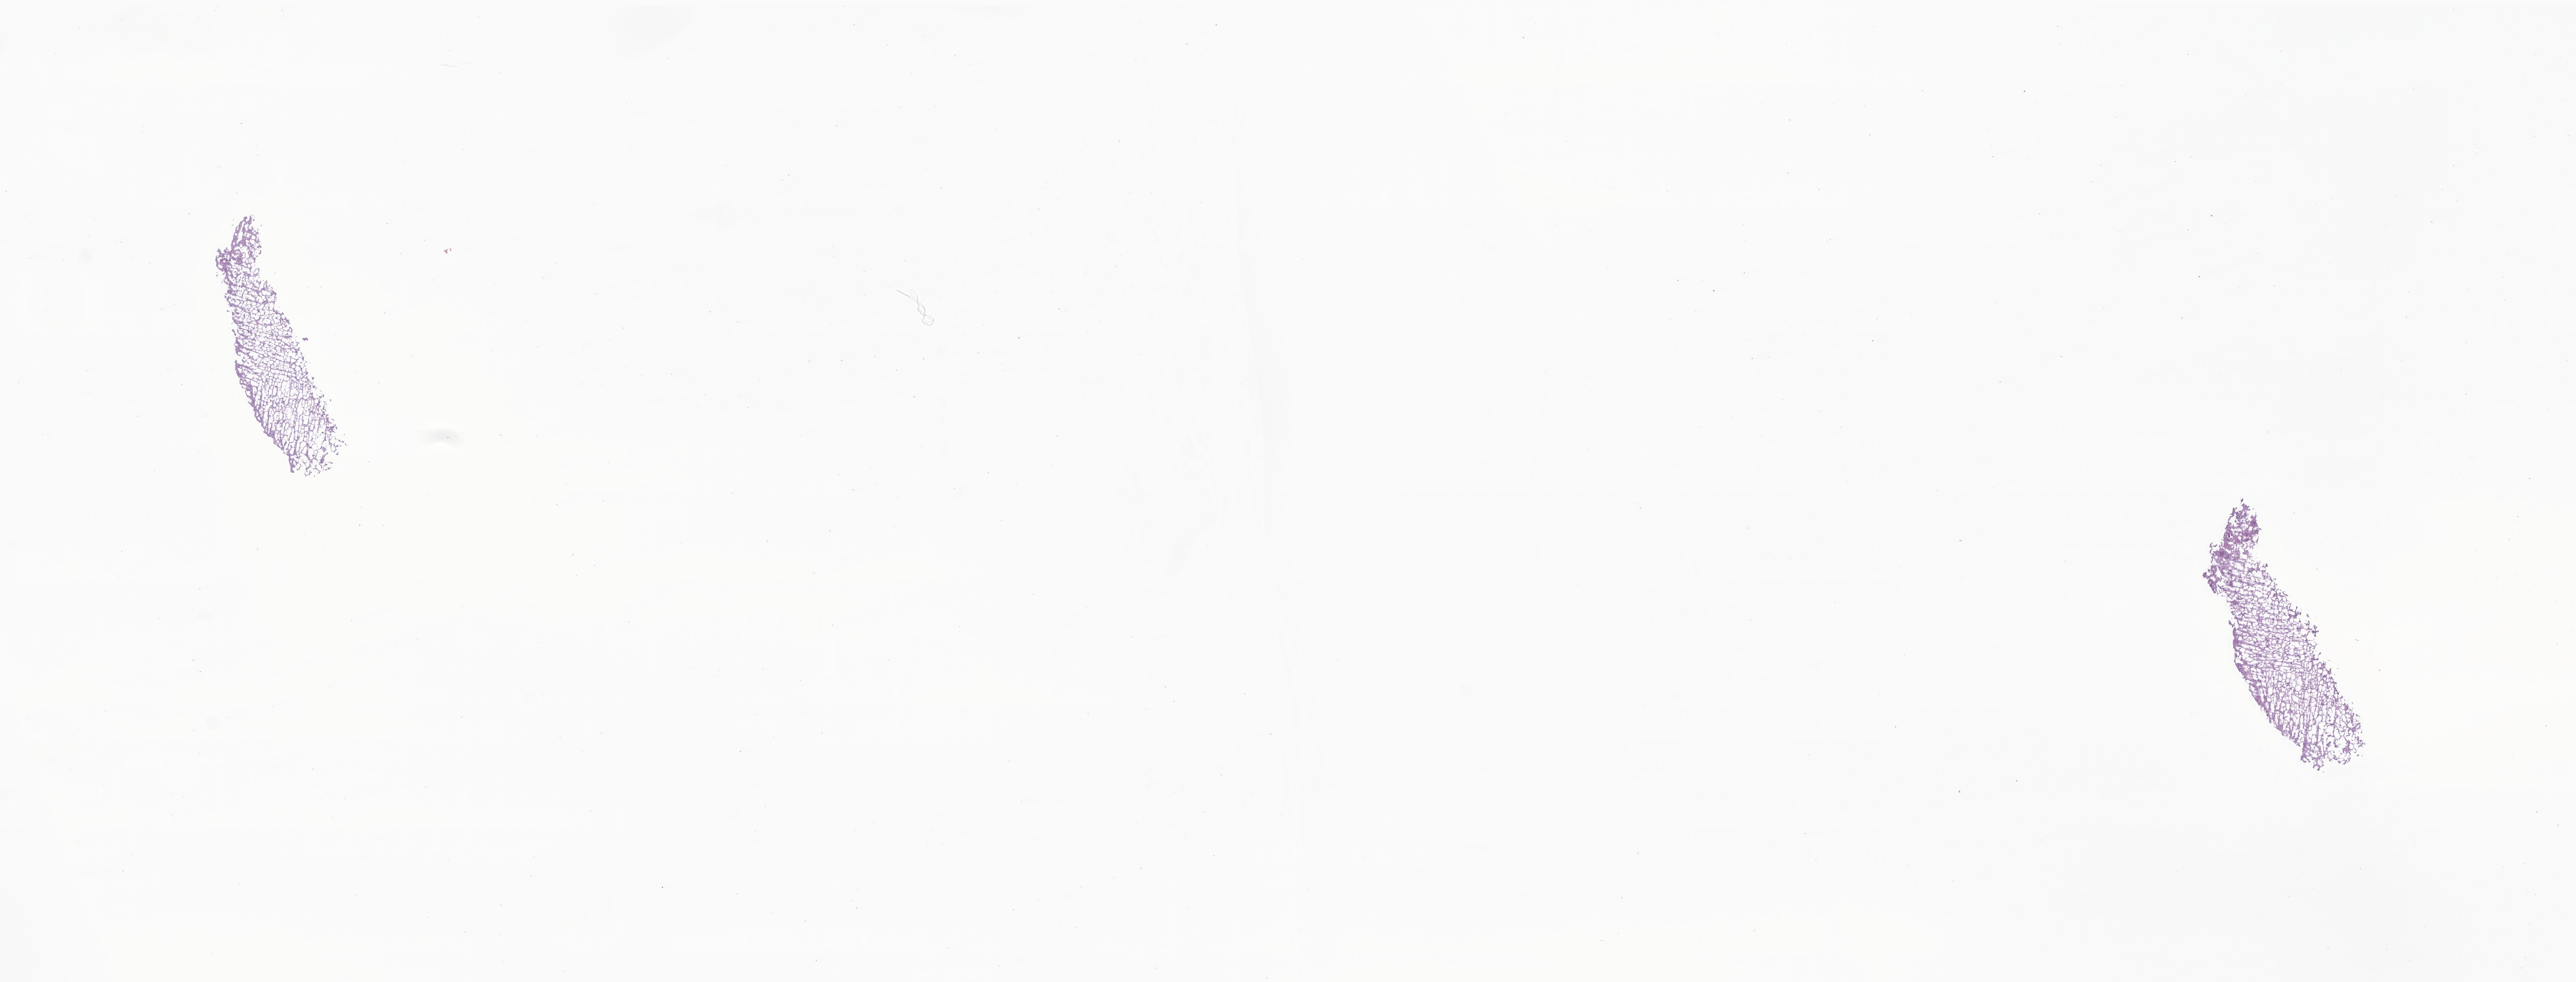
H&E whole-slide image of tumor tissue from the brain — whole scanned area (about 22.2 x 8.5 mm) shown as a low-resolution overview. Frozen section (OCT-embedded). Female patient, age 958 days (about 2.6 years).
Diagnosis (ICD-O-3 morphology term): Ependymoma, NOS.